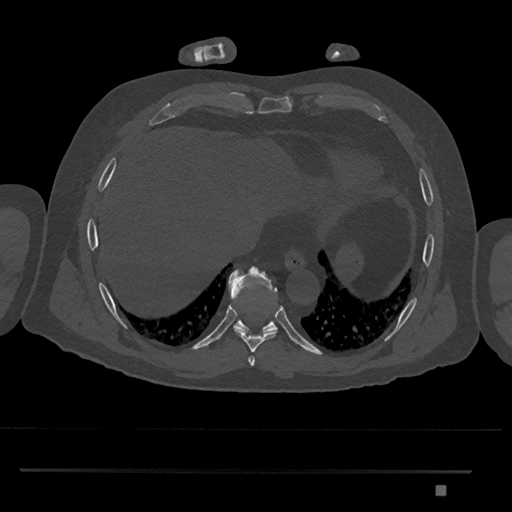
CT including the spine, one axial slice. Position 1087 of 1134 along the scan axis. Bone window (W 1800 / L 400 HU). 512 × 512 image matrix. Male patient, age 65 years. Case-level facts recorded for this patient, not image findings: primary cancer: prostate.
Outlined on this slice (semi-automatic segmentation, software-assisted and operator-edited):
- T8 vertebra: box from (x=234, y=309) to (x=277, y=352) px
- T9 vertebra: (x=228, y=266)–(x=278, y=333)